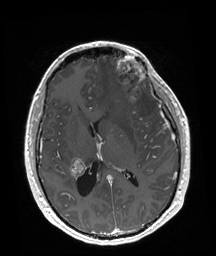
Brain MRI from a brain-tumour surgery series, one axial slice. Slice 88 of 192 in the series (ordered by position). T1-weighted post-contrast. 1 mm slice thickness. 216 × 256 image matrix, field of view 219 × 260 mm.
Structures marked on this image (outlined manually by an expert reader):
- tumour: box from (x=115, y=55) to (x=146, y=101) px